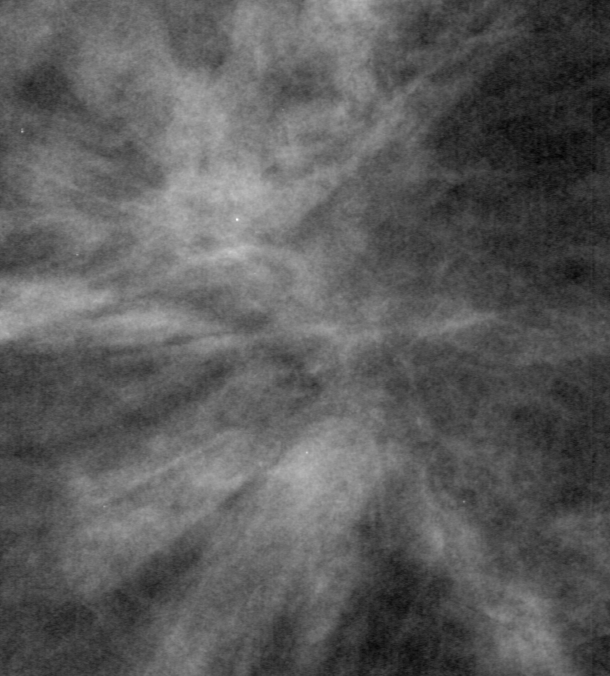
Cropped region of a digitized screen-film mammogram centred on a radiologist-marked abnormality; left breast; CC view.
Mass, shape architectural distortion, margins spiculated; BI-RADS assessment category 5; subtlety rating 5 on a 1 (subtle) to 5 (obvious) scale; pathology (as recorded): malignant.